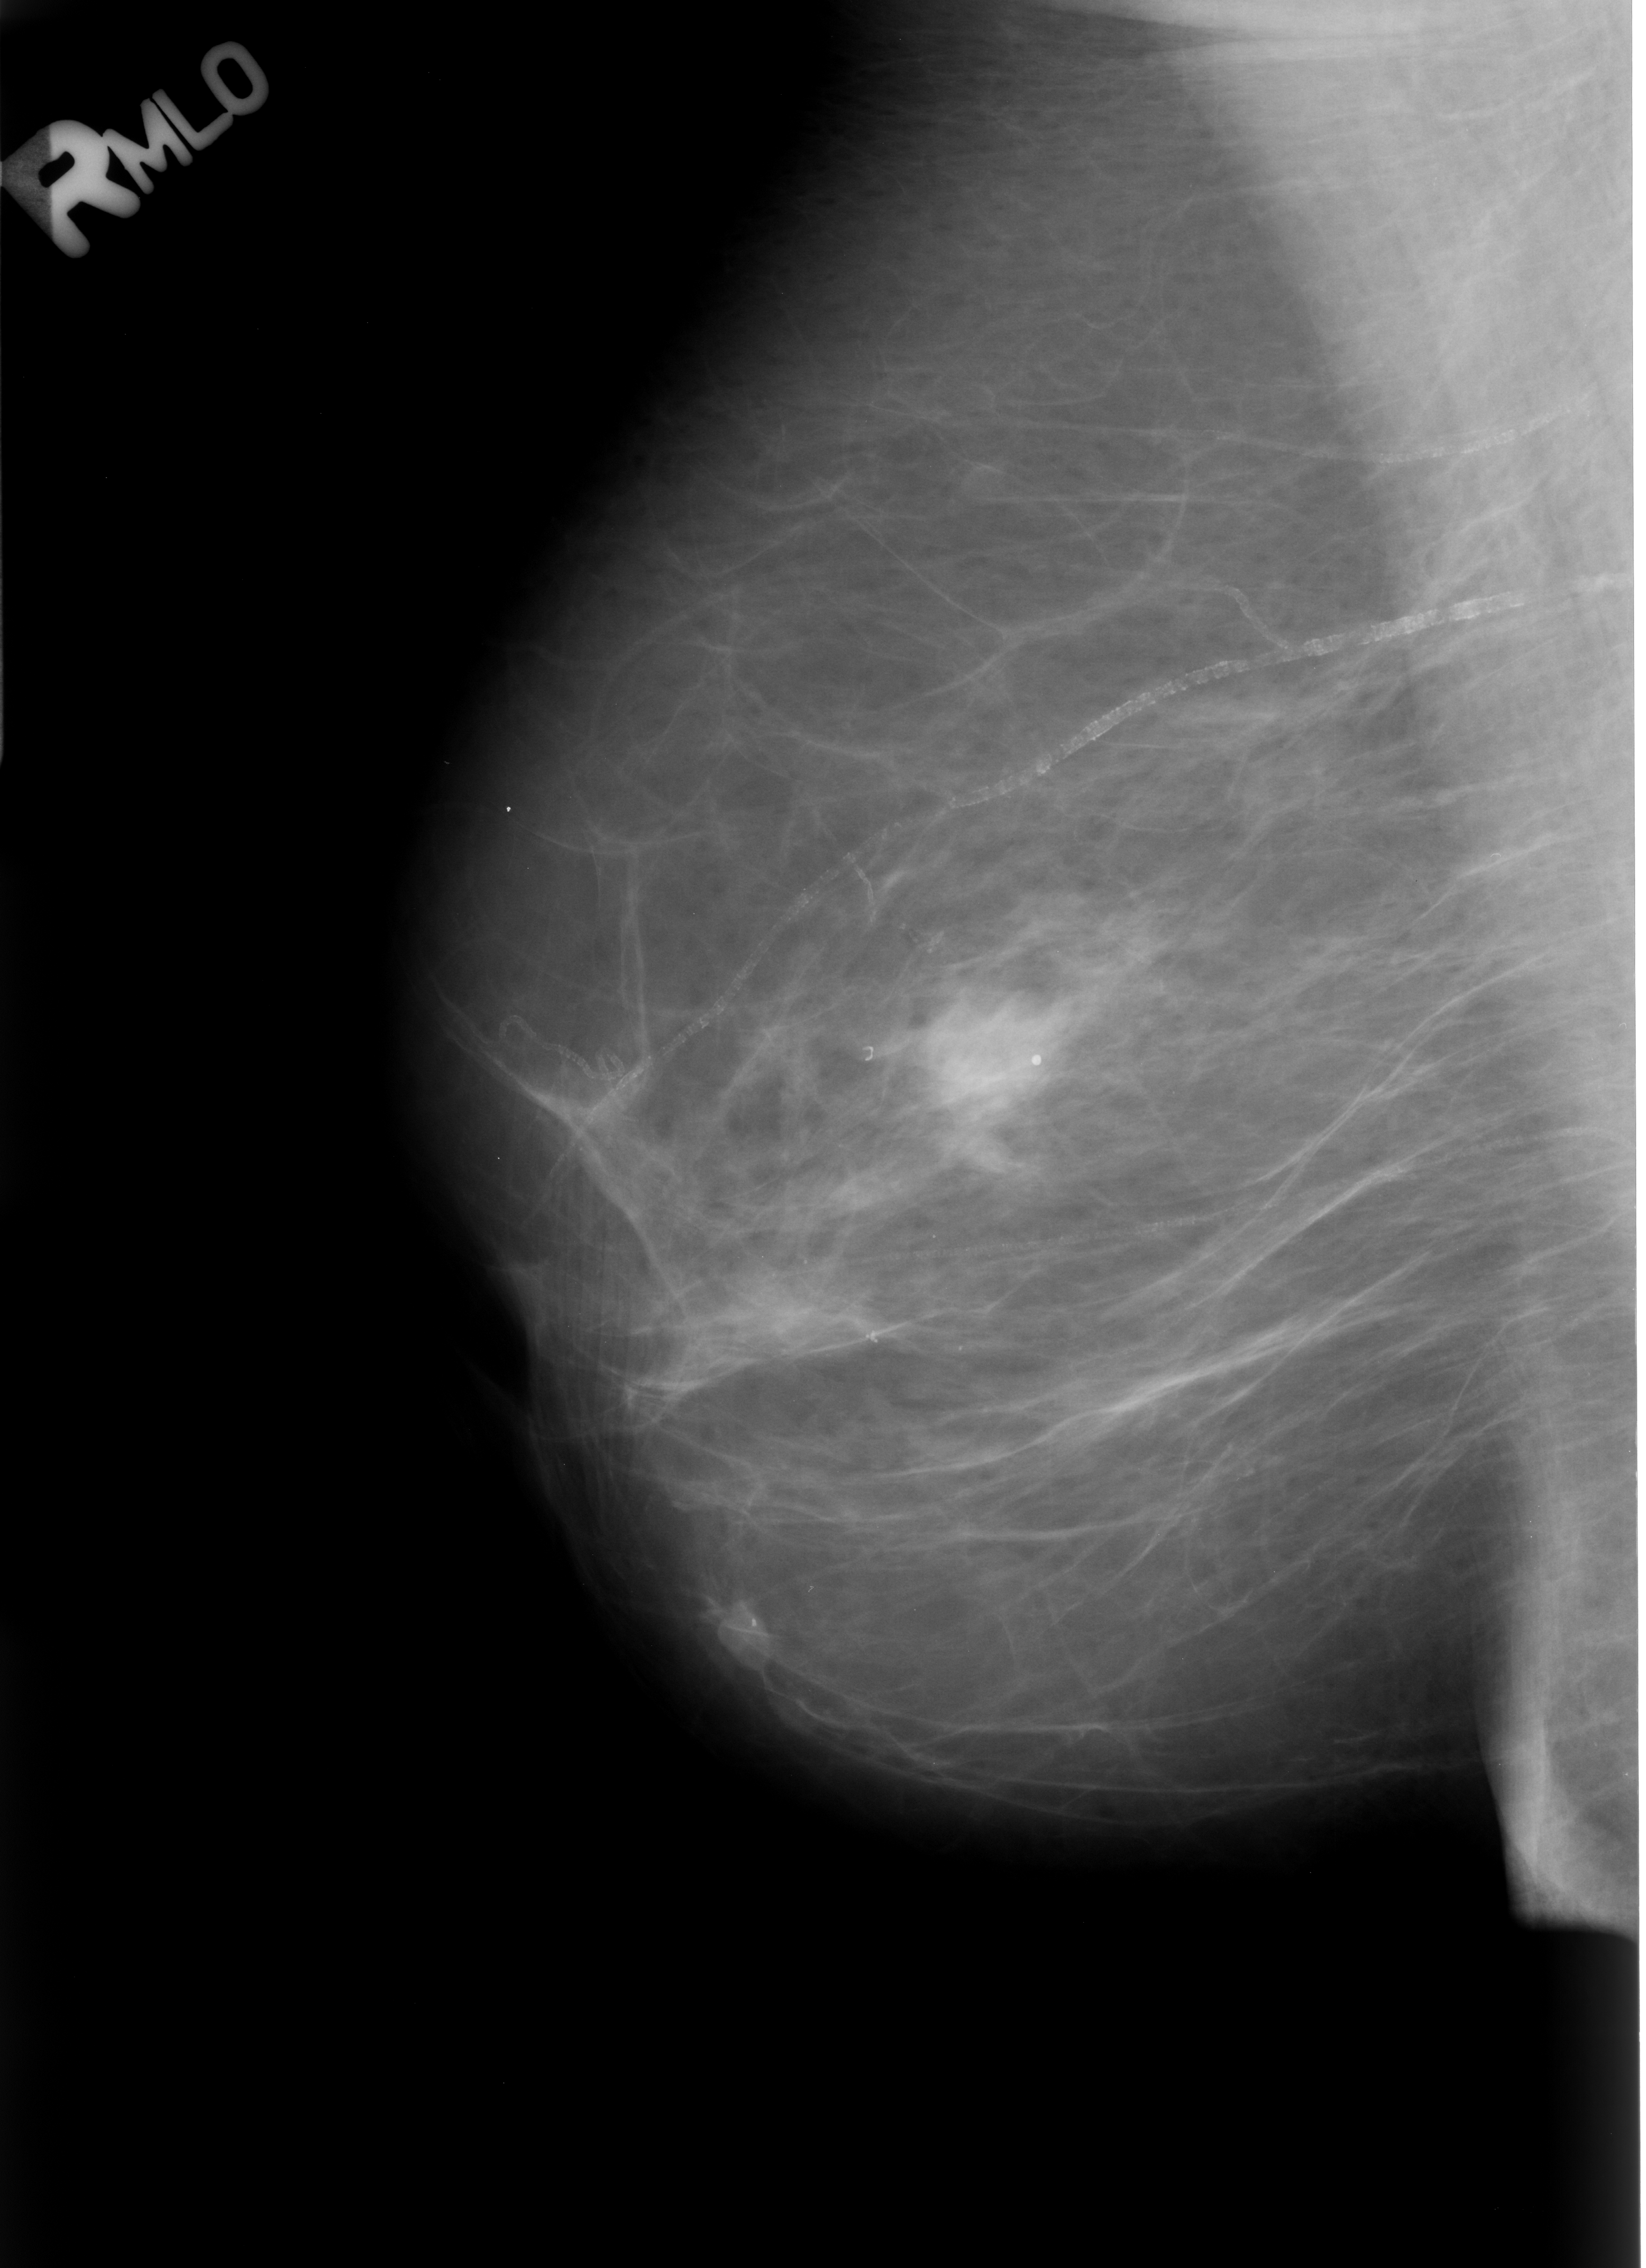
Digitized screen-film mammogram, right breast, mediolateral oblique (MLO) view, BI-RADS breast density category 2 (scale 1–4).
Marked findings (only marked abnormalities are described; nothing is implied about the rest of the image): mass, shape asymmetric breast tissue; BI-RADS assessment category 2; benign; no additional work-up was recommended (benign without callback).